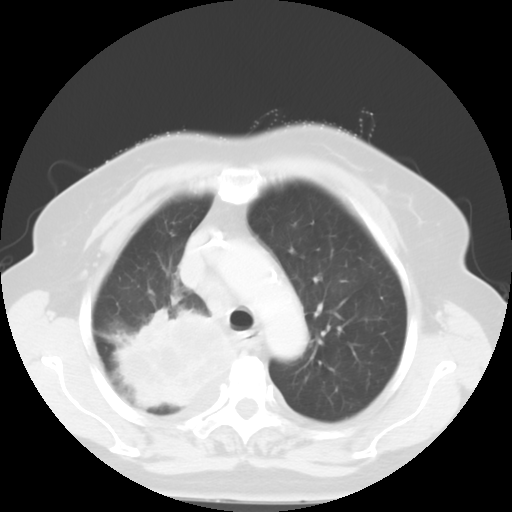
Chest CT, one axial slice. Slice 40 of 52 in the series (ordered by position). Reconstruction kernel STANDARD. 120 kVp. Lung window (W 1500 / L -600 HU). 512 × 512 image matrix, field of view 333 × 333 mm. Female patient, age 81 years. Case-level facts recorded for this patient, not image findings: clinical TNM (as recorded): T4 N3 M1b.
Annotated regions visible in this slice (bounding box drawn by a radiologist):
- lung tumour (recorded histology: adenocarcinoma): bounding box [x1, y1, x2, y2] px = [115, 305, 234, 415]